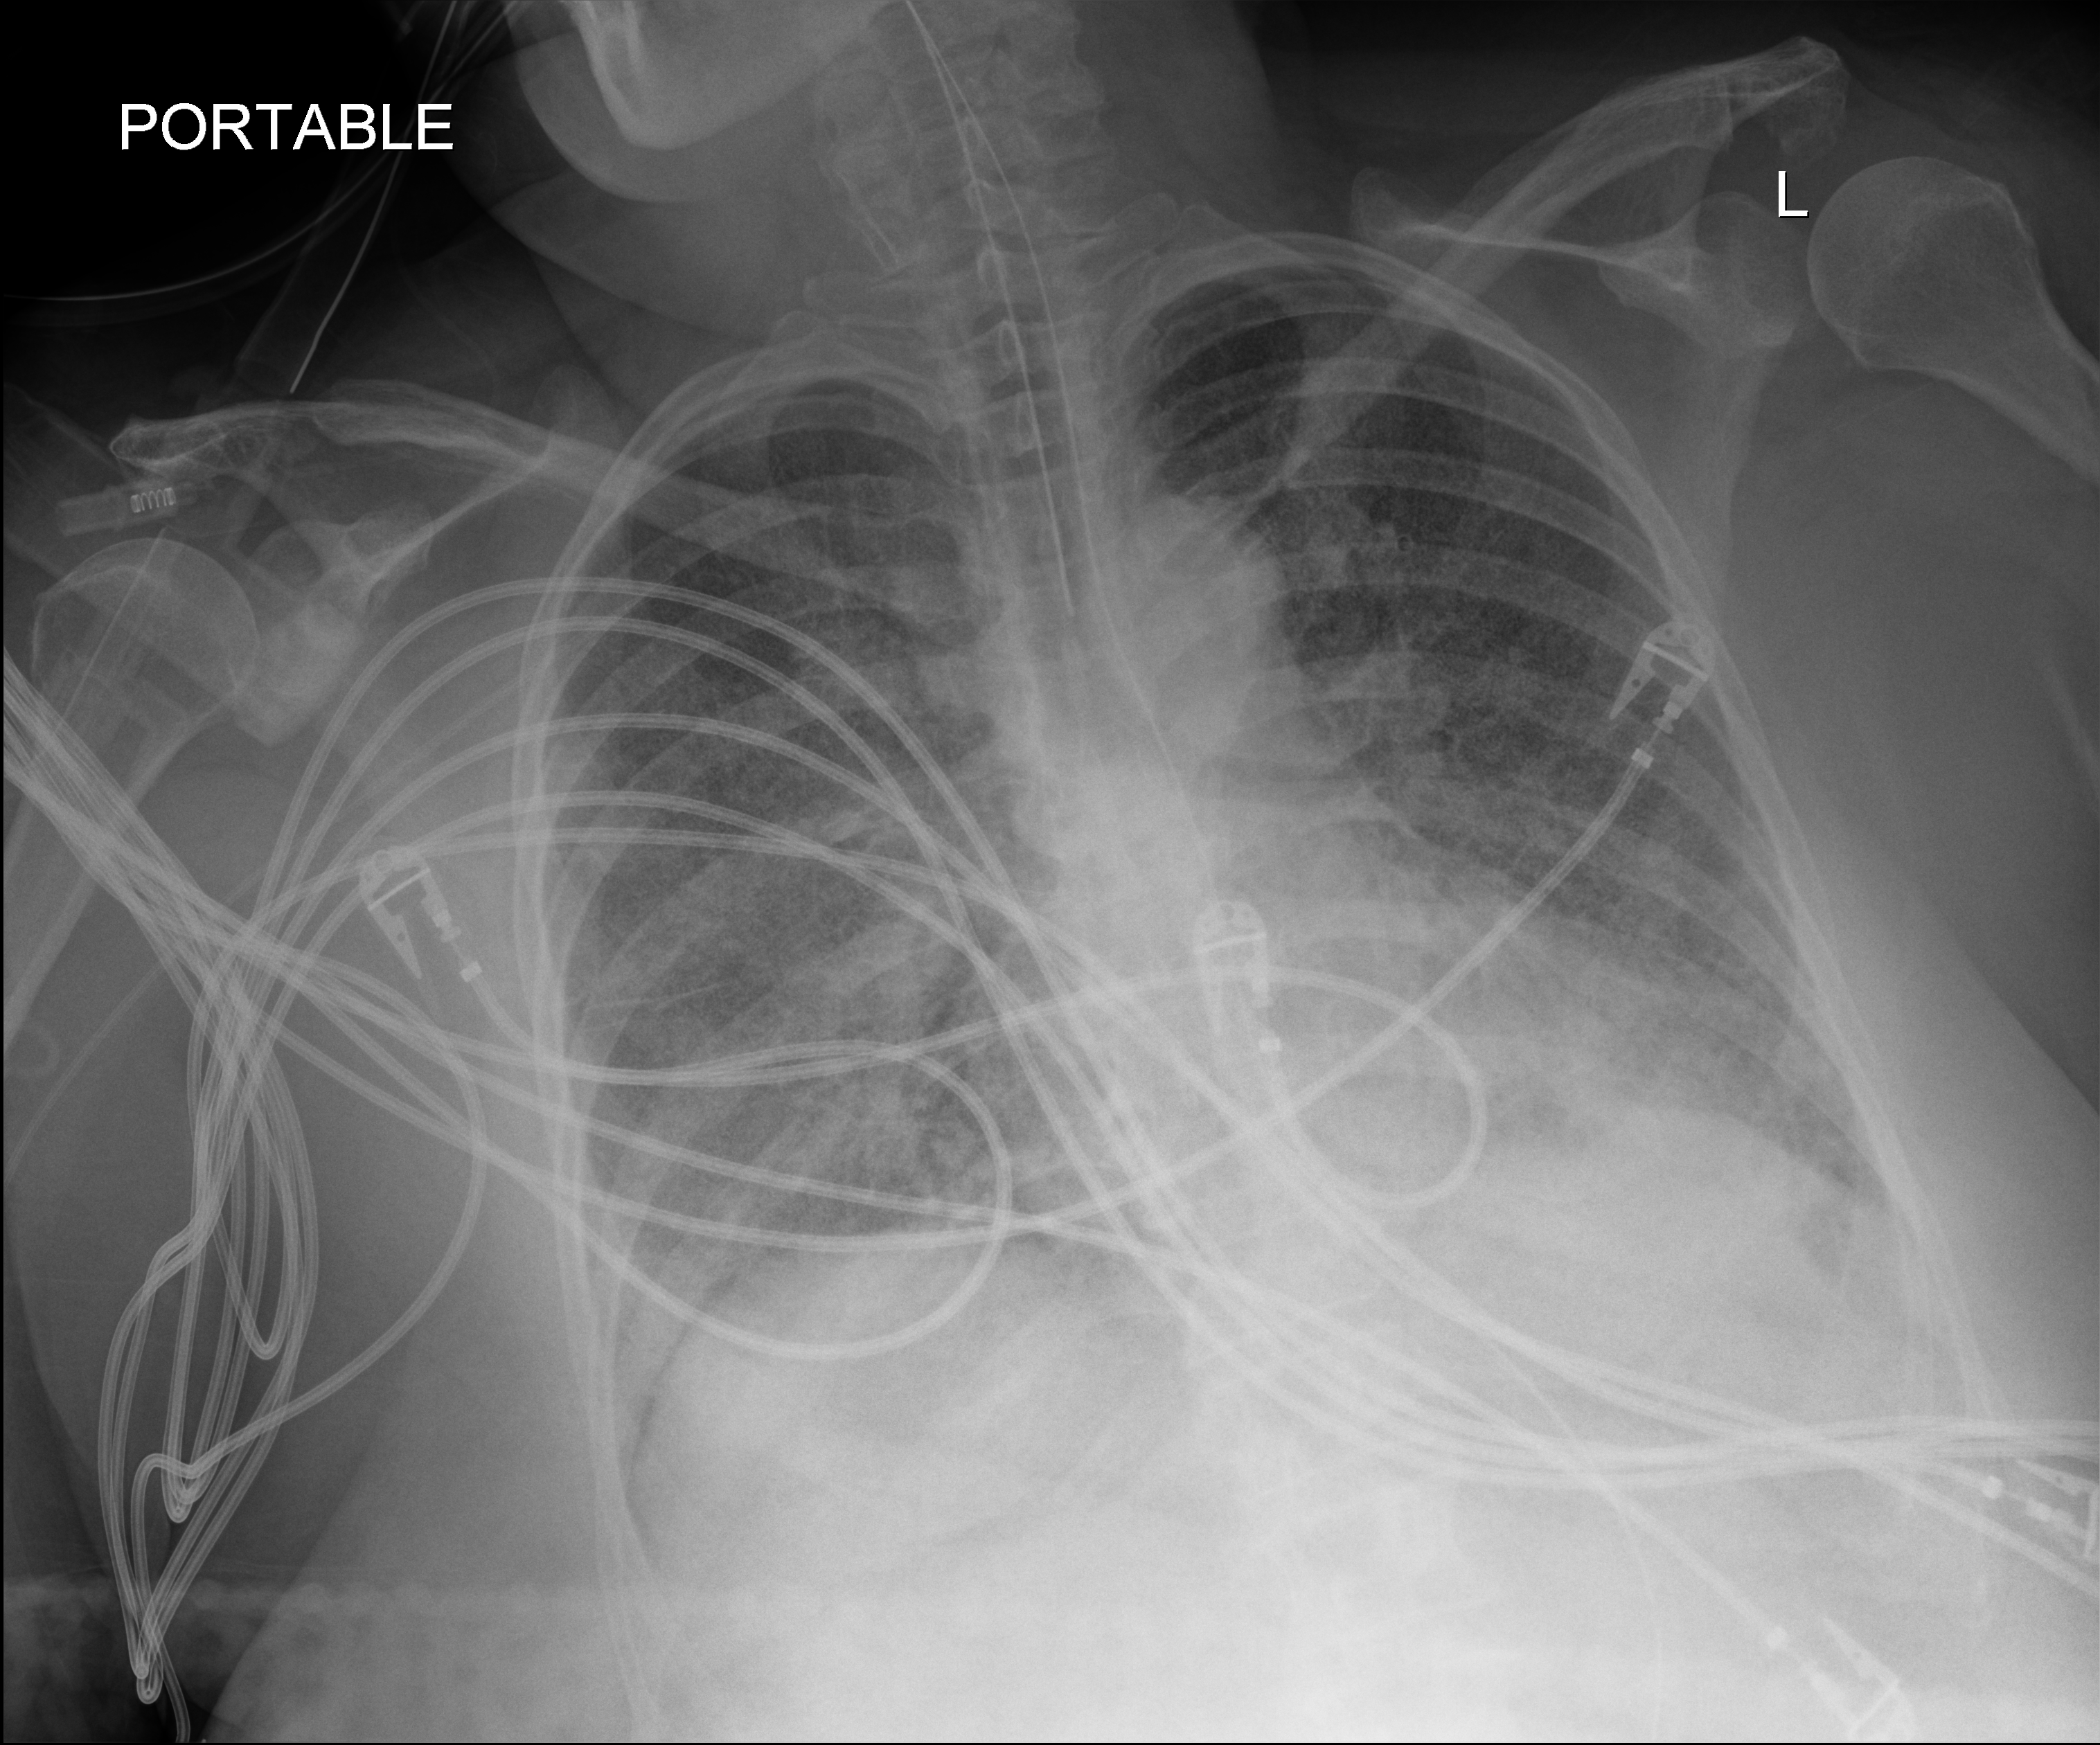
Bedside chest radiograph (digital radiography); anteroposterior (AP) projection. Patient hospitalised with COVID-19; female, aged 60–74 years.
Admission-level facts for this patient (not findings on this image; timing relative to this image not recorded): chronic kidney disease (admission record): no; mechanically ventilated during this hospital stay: yes.